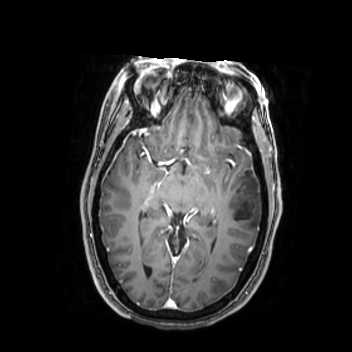
Brain MRI from a brain-tumour surgery series, one axial slice; position 151 of 350 along the scan axis; T1-weighted post-contrast; 0.9 mm slice thickness; 352 × 352 image matrix, field of view 280 × 280 mm. From the clinical record (not read from this slice): histopathology: Oligodendroglioma; WHO grade: 2; IDH mutation: yes; tumour location: Left Middle Temporal Gyrus.
Annotated regions visible in this slice (manually delineated by an expert):
- tumour: bounding box <224,175,262,233> (left, top, right, bottom; pixels)